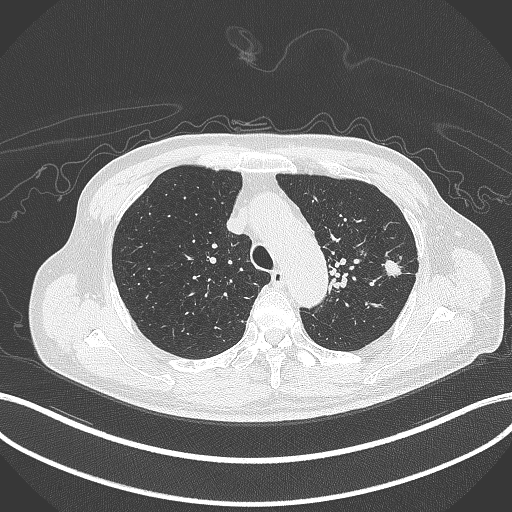
Chest CT, one axial slice; slice 334 of 417 in the series (ordered by position); reconstruction kernel B70f; 120 kVp; lung window (W 1500 / L -600 HU); 1 mm slice thickness; 512 × 512 image matrix, field of view 400 × 400 mm. Male patient, age 77 years. Case-level facts recorded for this patient, not image findings: clinical TNM (as recorded): T3 N1 M0.
Outlined on this slice (rectangle marked by the reading radiologist):
- lung tumour (recorded histology: adenocarcinoma): bounding box [x1, y1, x2, y2] px = [382, 257, 405, 279]